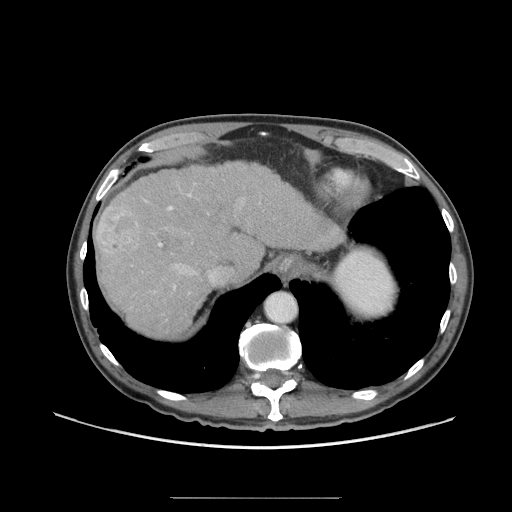
Contrast-enhanced abdominal CT (liver protocol), one axial slice. Reconstruction kernel STANDARD. 140 kVp. Soft-tissue window (W 400 / L 40 HU). 2.5 mm slice thickness. 512 × 512 image matrix, field of view 400 × 400 mm. Case-level facts recorded for this patient, not image findings: diagnosis: hepatocellular carcinoma (patient treated with transarterial chemoembolisation; whether this scan precedes or follows treatment is not stated here); TNM stage (as recorded): Stage-I; Child-Pugh class: A; tumour nodularity: uninodular; tumour size: 3.5 cm.
Annotated regions visible in this slice (semi-automatic segmentation, software-assisted and operator-edited):
- abdominal aorta: bounding box (x1, y1, x2, y2) in pixels: (266, 293, 297, 323)
- liver parenchyma outside the tumour (the mass and vessels are separate outlines, so this box may not span the whole liver): (94, 160, 344, 338)
- mass: (96, 206, 147, 262)
- liver vessels: (145, 194, 216, 290)